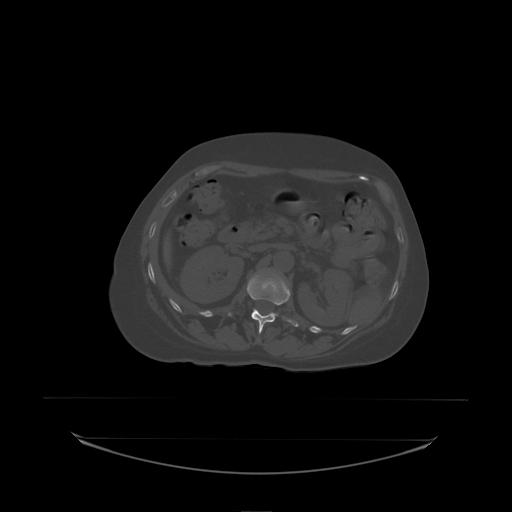
CT including the spine, one axial slice; slice 82 of 242 in the series (ordered by position); bone window (W 1800 / L 400 HU); 2.5 mm slice thickness; 512 × 512 image matrix, field of view 500 × 500 mm. Female patient, age 53 years. Case-level facts recorded for this patient, not image findings: primary cancer: lung; vertebrae with lytic lesions (as recorded): T7, L1.
Annotated regions visible in this slice (semi-automatically segmented with operator editing):
- L1 vertebra: bounding box (x1, y1, x2, y2) in pixels: (229, 274, 299, 334)